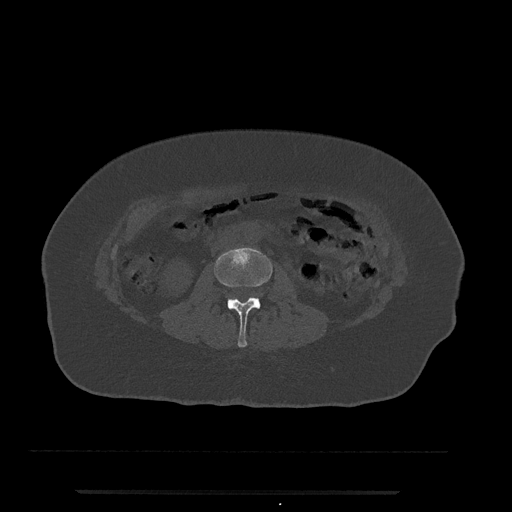
CT including the spine, one axial slice. Slice 20 of 797 in the series (ordered by position). Reconstruction kernel Br40s/3. 120 kVp. Bone window (W 1800 / L 400 HU). 0.5 mm slice thickness. 512 × 512 image matrix. Female patient, age 51 years. From the clinical record (not read from this slice): primary cancer: neuro.
Annotated regions visible in this slice (semi-automatically segmented with operator editing):
- L2 vertebra: bounding box <214,247,273,347> (left, top, right, bottom; pixels)